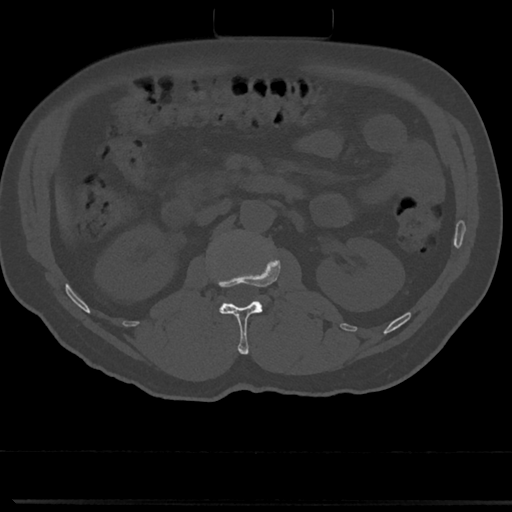
CT including the spine, one axial slice; slice 60 of 817 in the series (ordered by position); reconstruction kernel Br40s/3; 120 kVp; bone window (W 1800 / L 400 HU); 0.5 mm slice thickness; 512 × 512 image matrix, field of view 355 × 355 mm. Patient: male, 61 years. Case-level facts recorded for this patient, not image findings: primary cancer: prostate.
Annotated regions visible in this slice (semi-automatic segmentation, software-assisted and operator-edited):
- L1 vertebra: box from (x=211, y=253) to (x=280, y=354) px